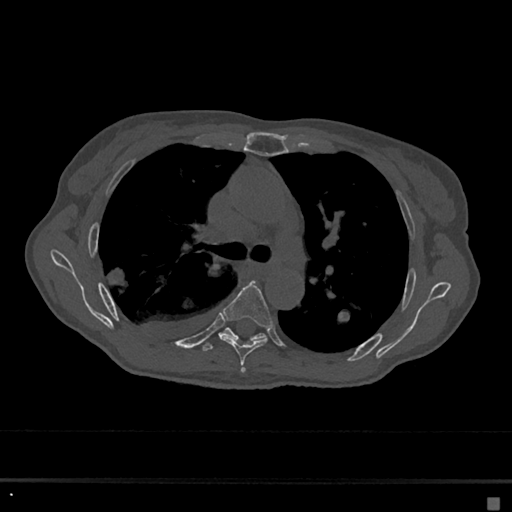
CT including the spine, one axial slice; position 449 of 797 along the scan axis; reconstruction kernel Br40s/3; bone window (W 1800 / L 400 HU); 0.5 mm slice thickness; 512 × 512 image matrix, field of view 360 × 360 mm. Female patient, age 68 years. Case-level facts recorded for this patient, not image findings: primary cancer: renal.
Outlined on this slice (semi-automatically segmented with operator editing):
- T5 vertebra: box from (x=222, y=280) to (x=273, y=373) px
- T6 vertebra: (x=202, y=327)–(x=266, y=352)